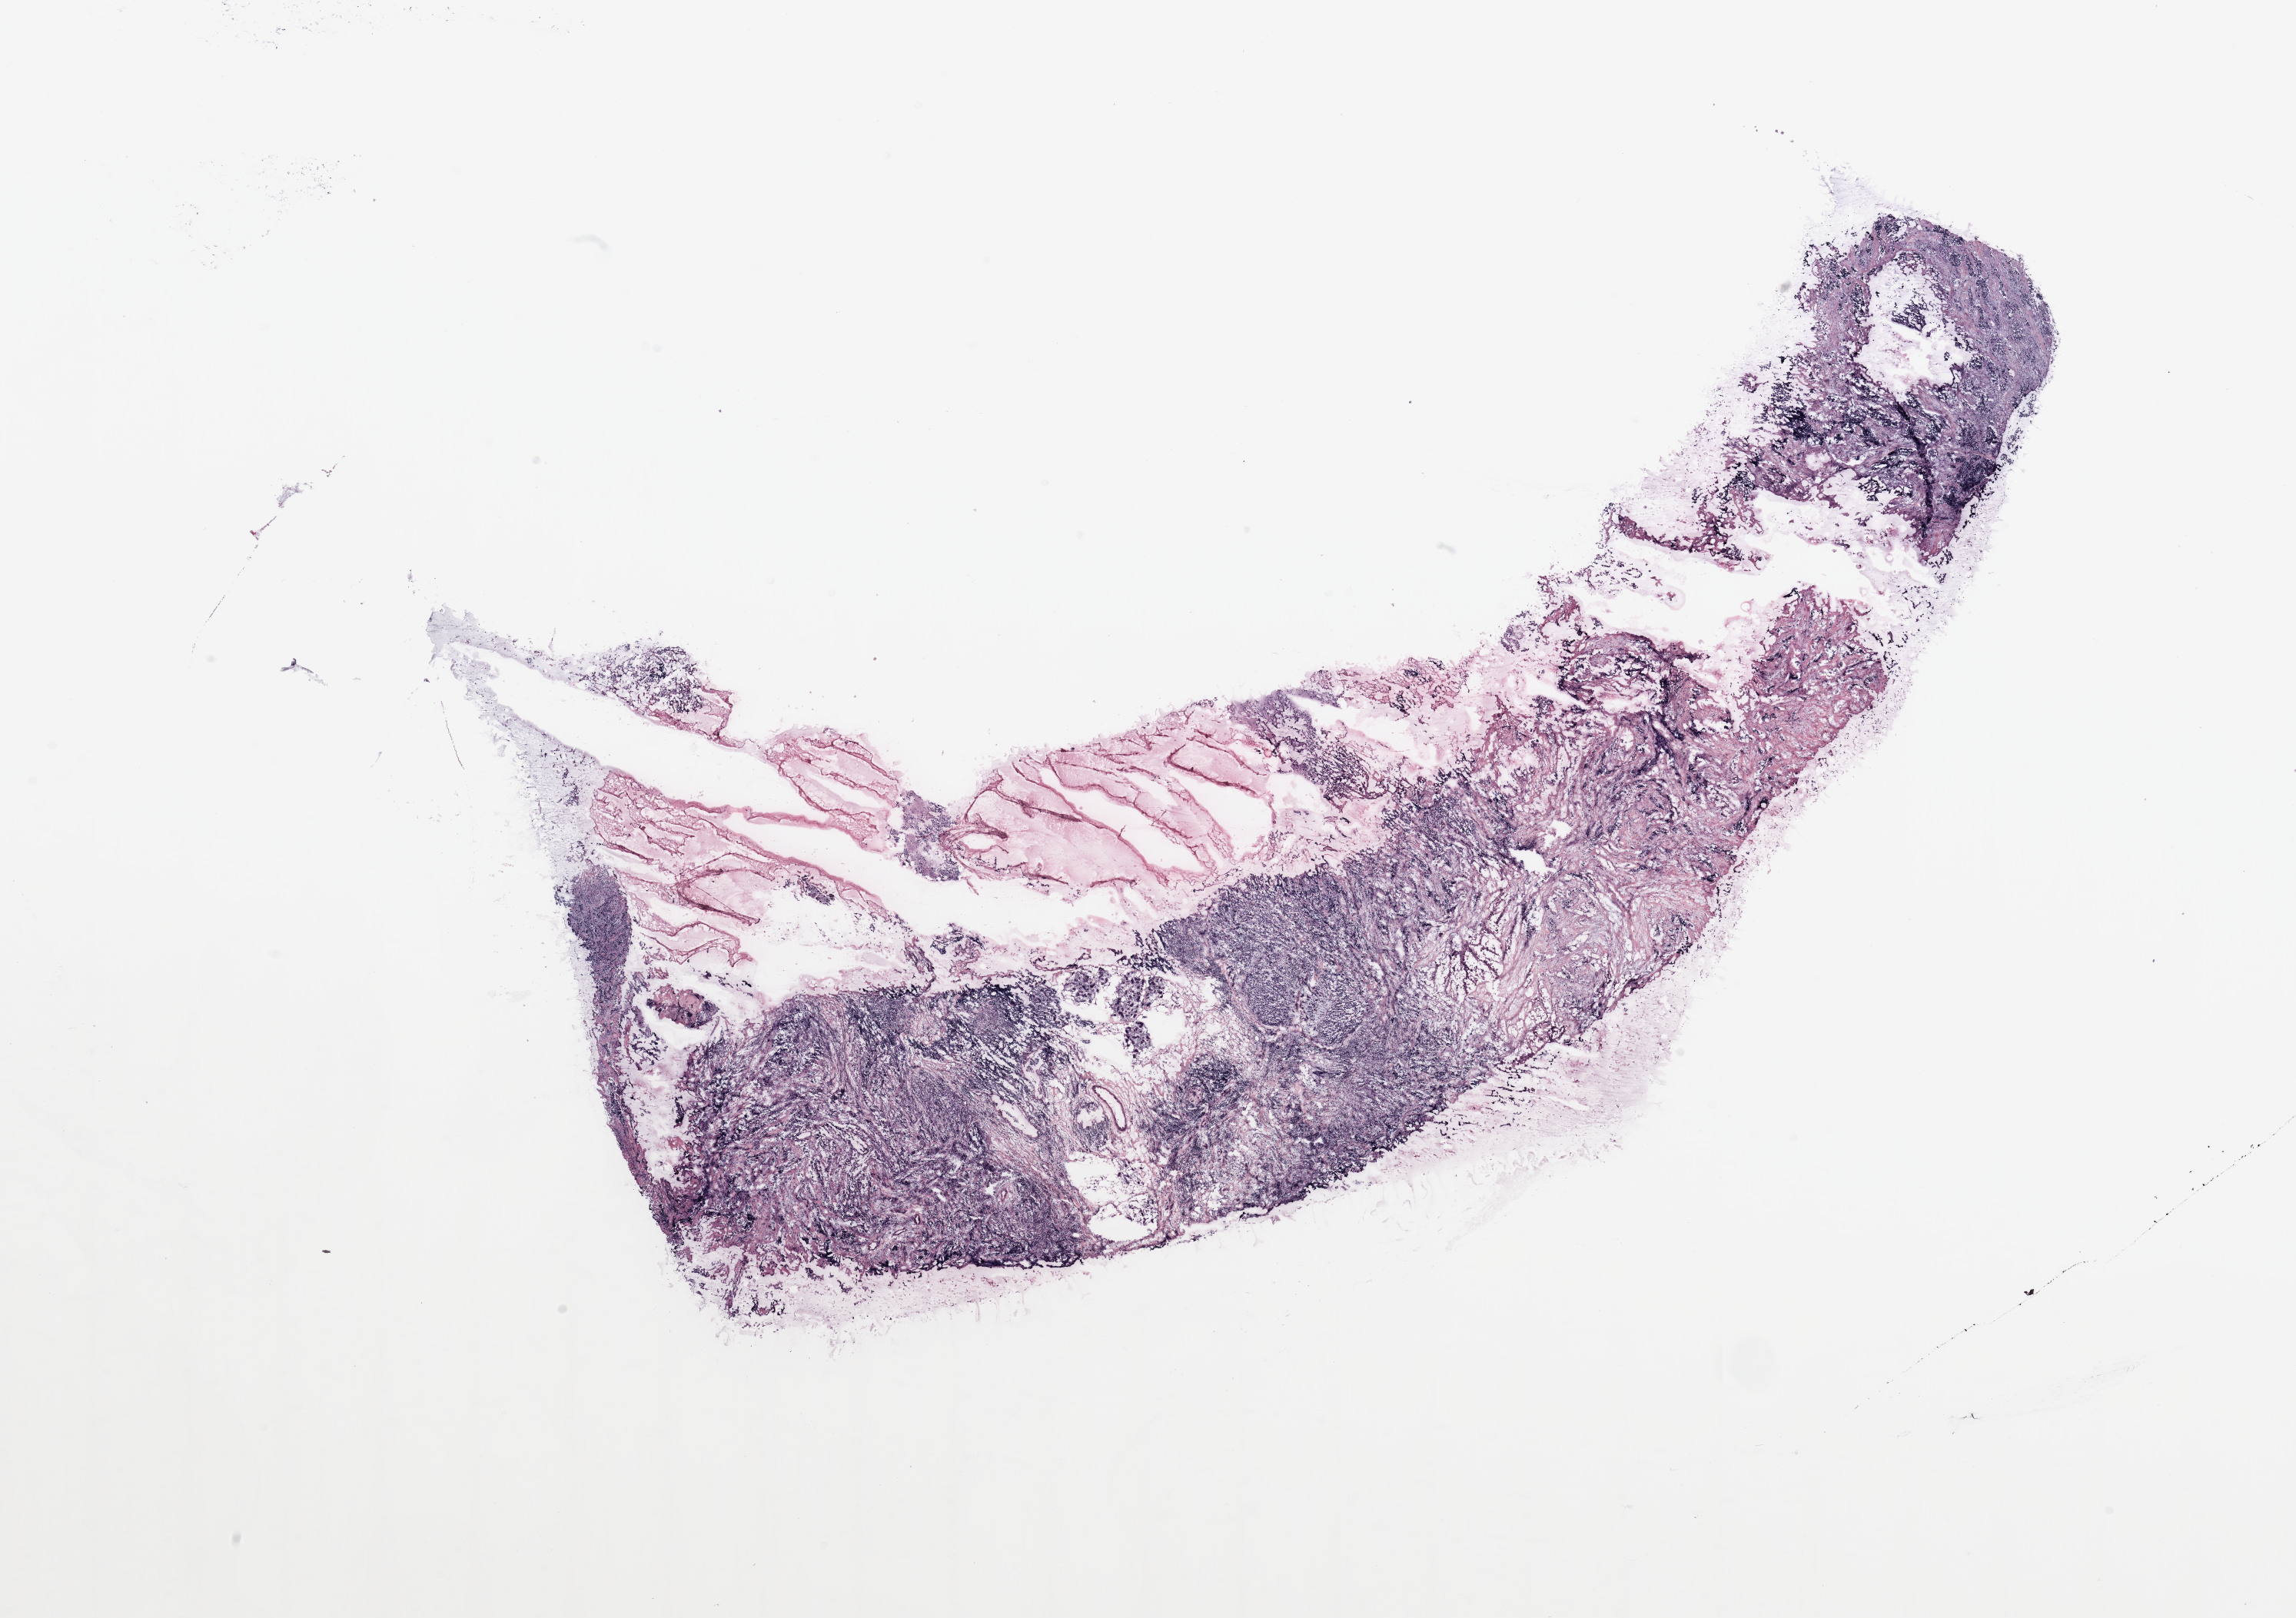
Whole-slide histology image, H&E, shown as a low-resolution overview of the whole scanned area (about 23.6 x 16.6 mm, acquisition: 20x scan). 45-year-old female patient.
Specimen: breast, tumour tissue.